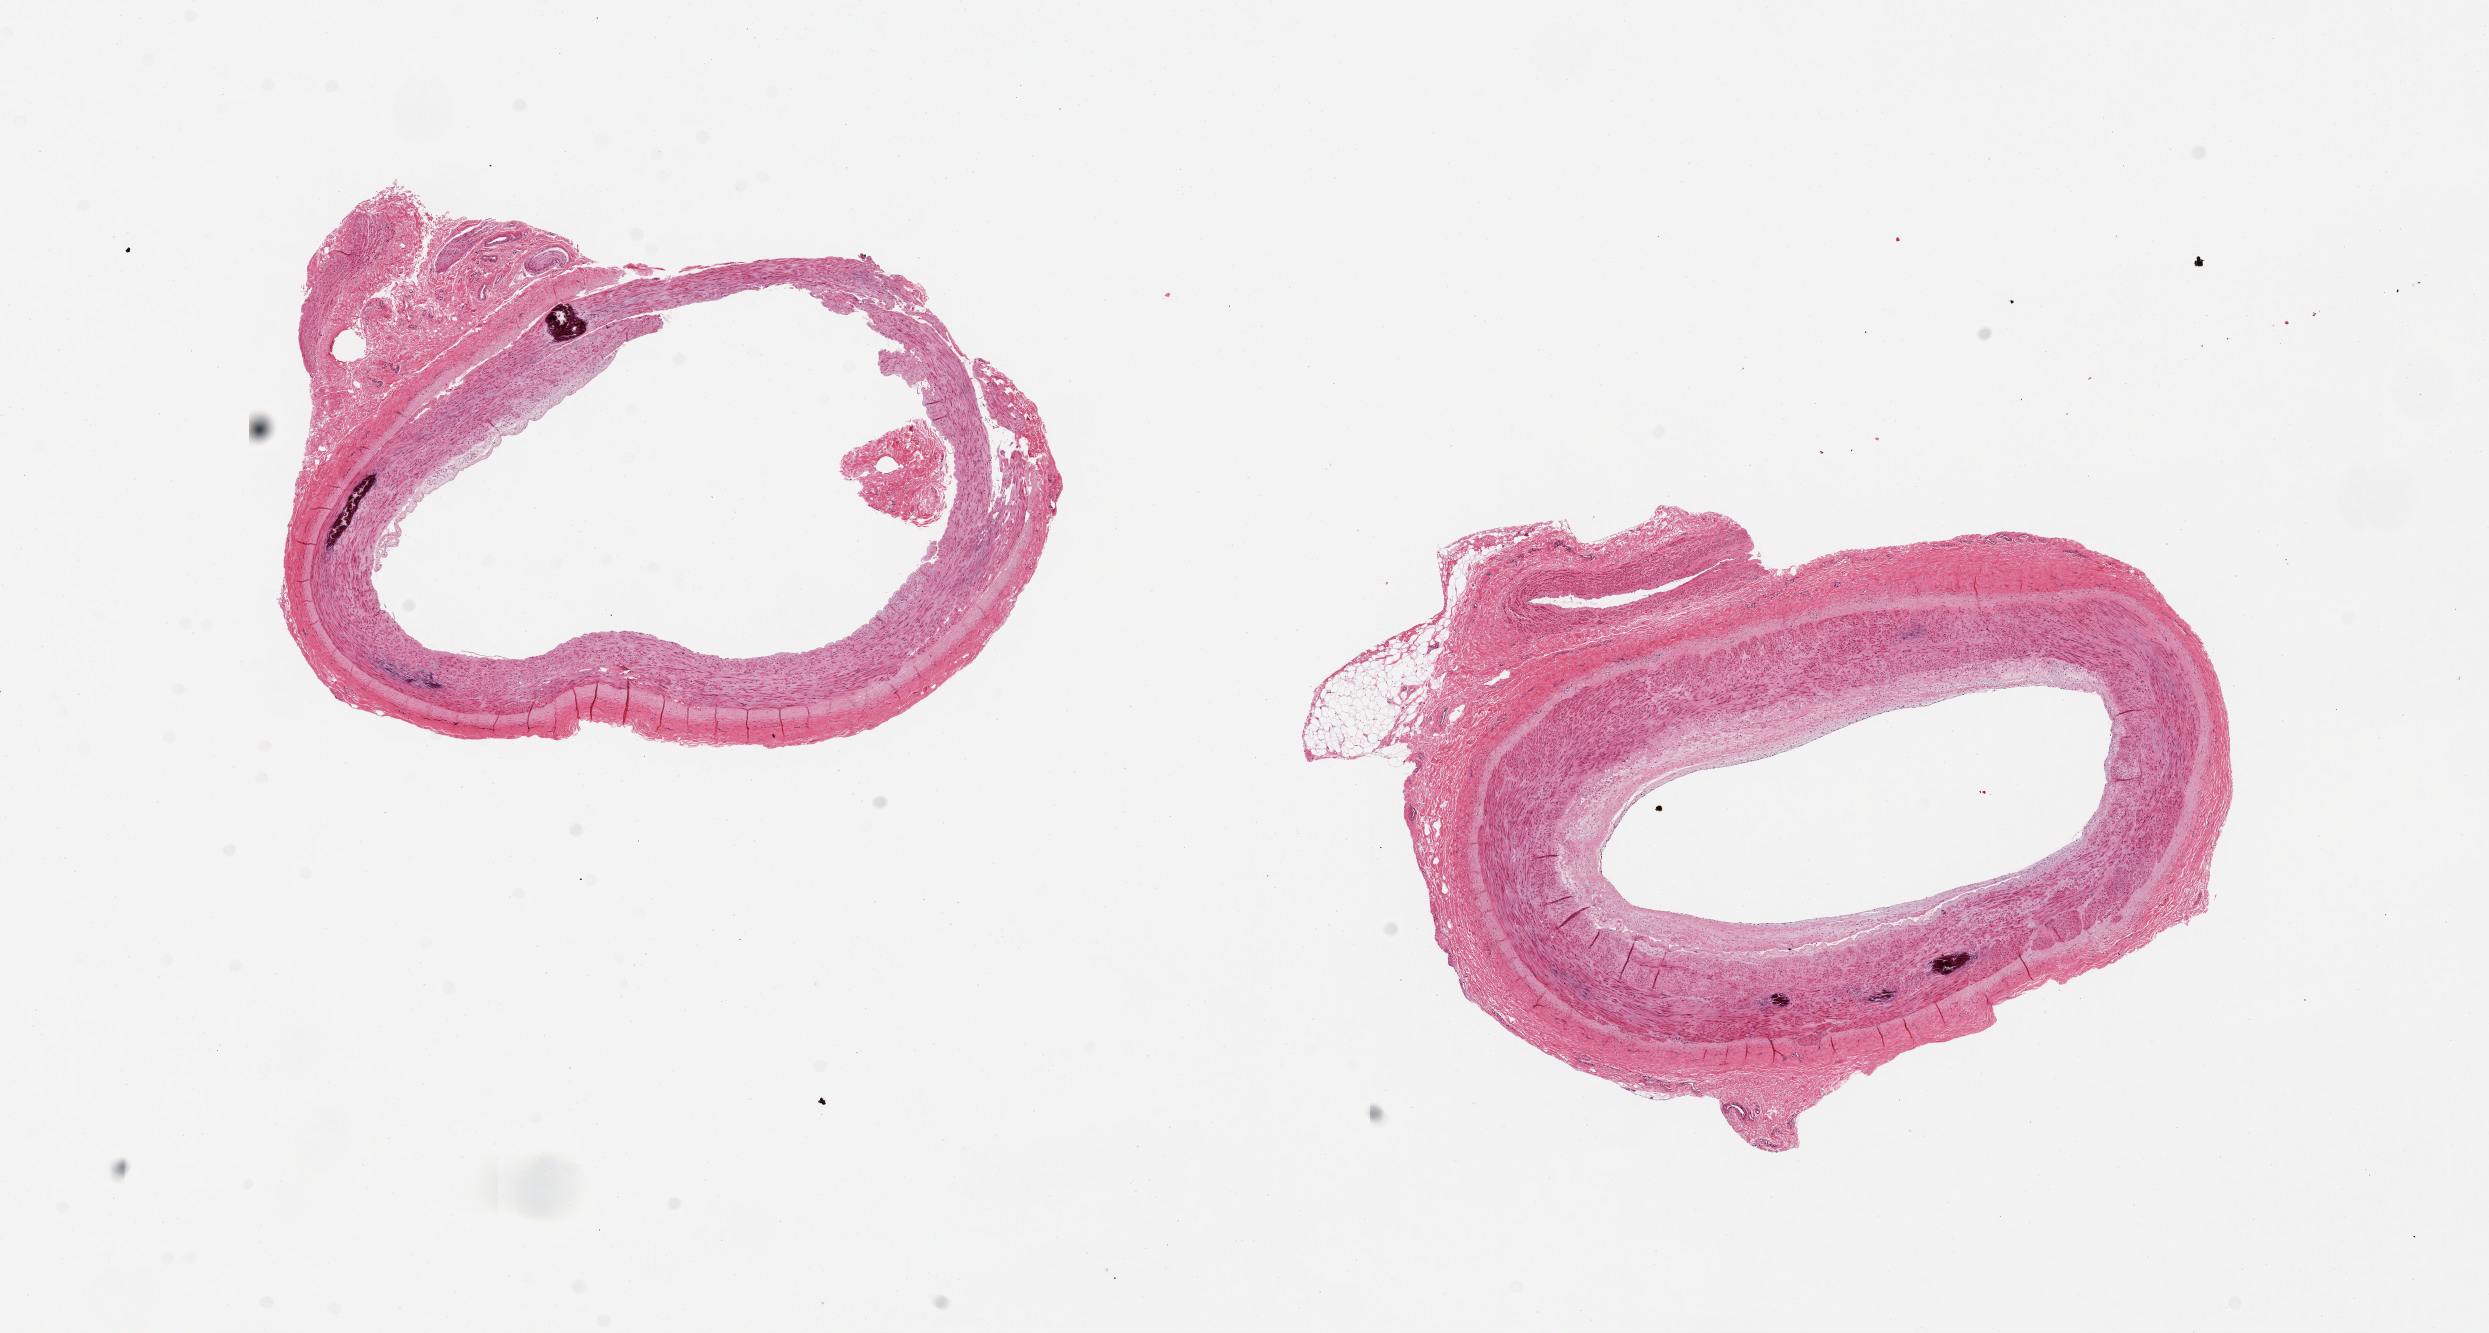
Digitized haematoxylin and eosin-stained section — low-resolution overview of the scanned area, about 19.7 x 10.5 mm (acquisition: 20x scan); PAXgene-fixed, paraffin-embedded tissue; target tissue: tibial artery; donor tissue sample.
Reviewer comment on this tissue sample: 2 pieces, 6x4.5 & 7x5mm; 1mm adherent fibrous &/or peripher al nerve on both.